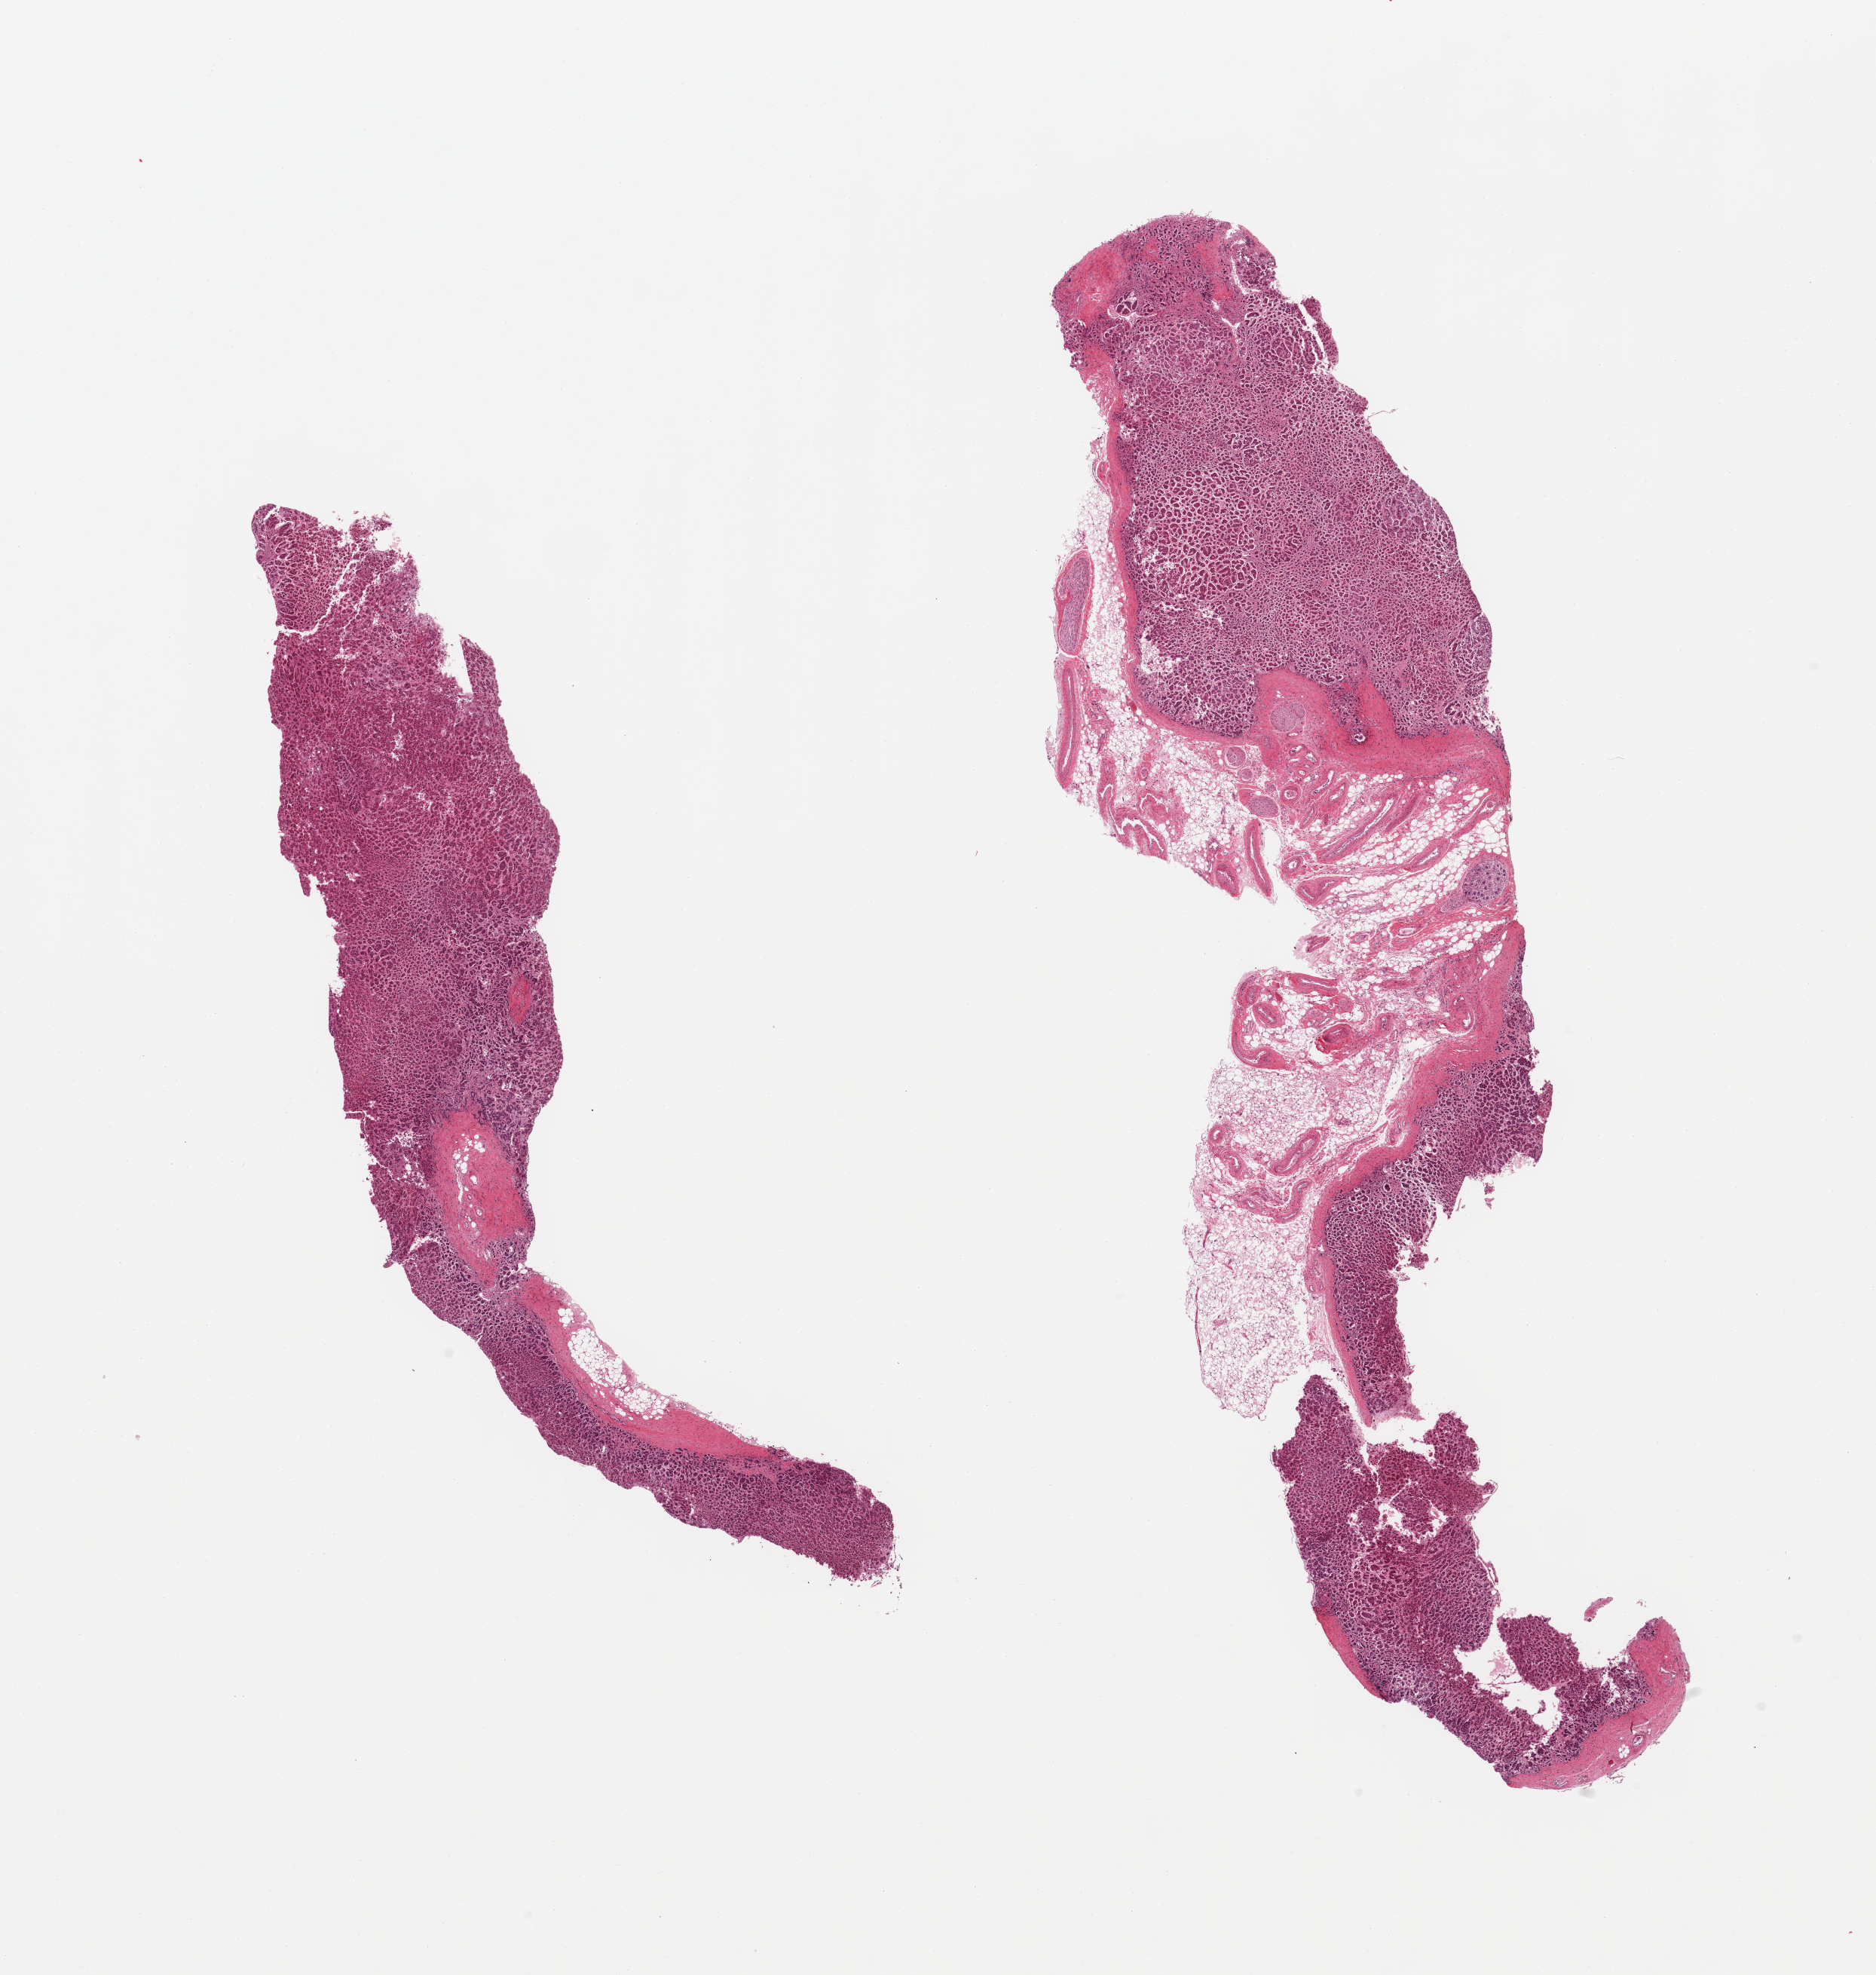
Whole-slide image, H&E stain, low-resolution overview of the scanned area, about 19.7 x 20.7 mm (slide scanned at 20x). PAXgene-fixed, paraffin-embedded tissue. Target tissue: adrenal gland. Tissue donor sample. Male donor.
- reviewer comment on this tissue sample: 2 pieces; larger piece has 50% external vascular & fatty content